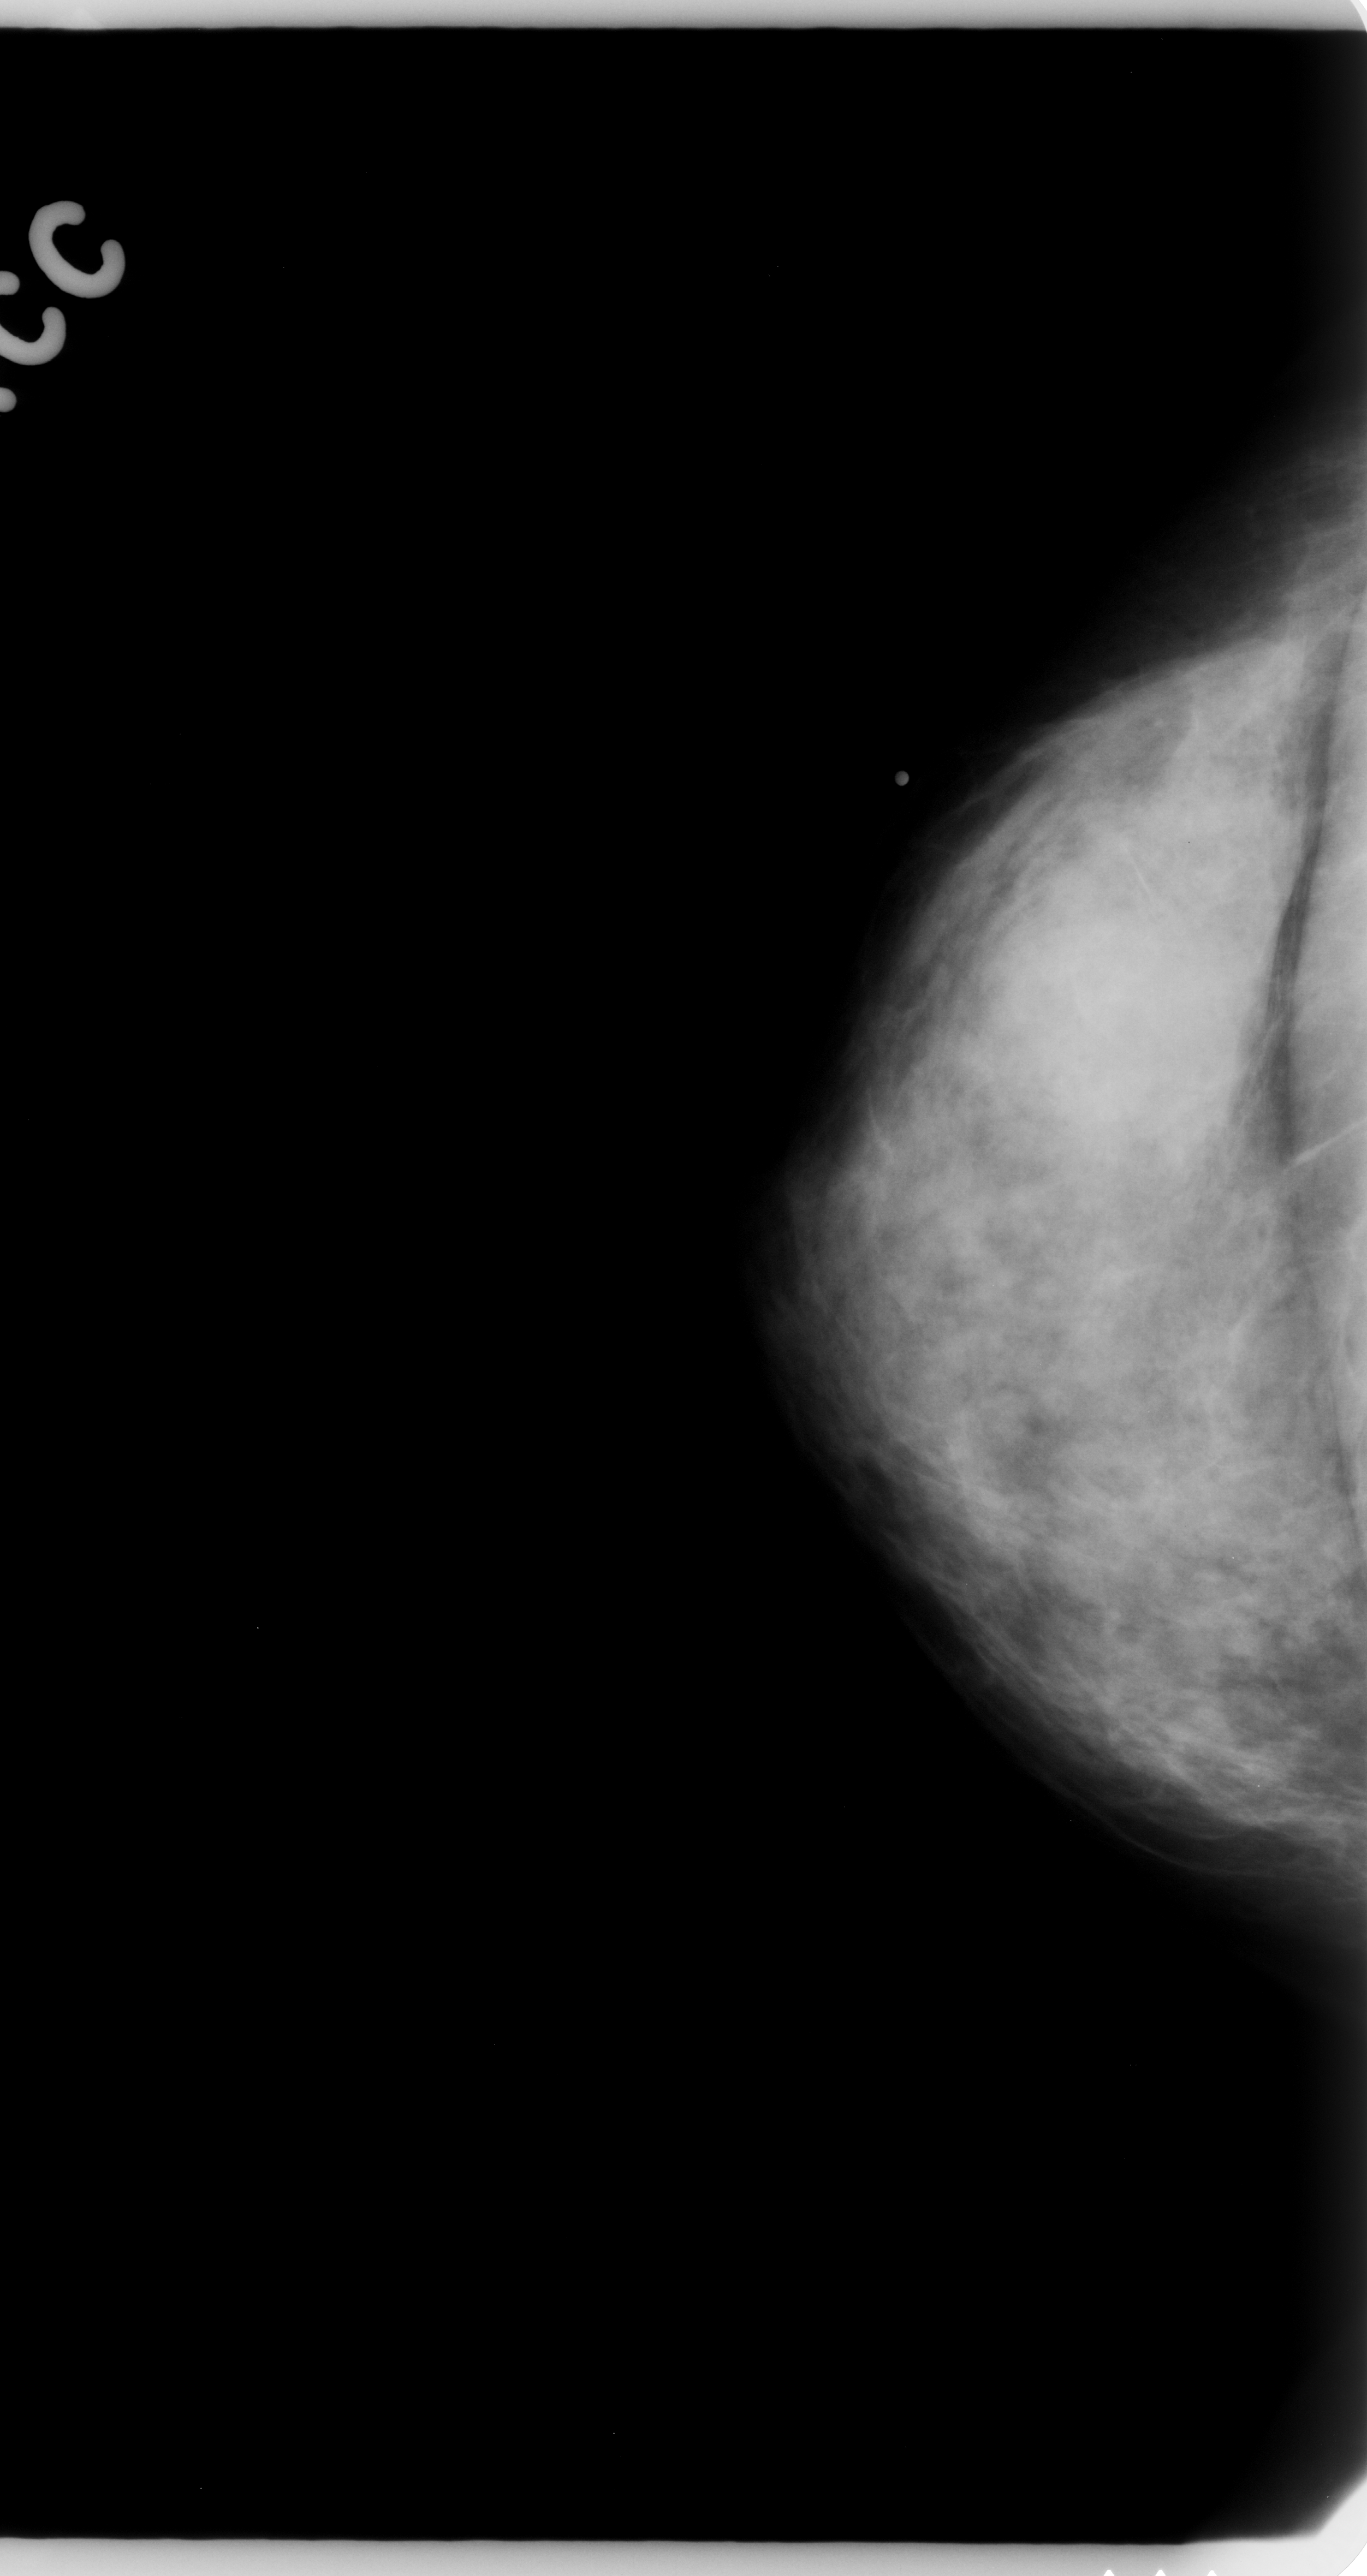
Mammogram (digitized film), right breast, CC view.
Abnormality record for this image: mass, shape round, margins ill defined; BI-RADS assessment category 4; pathology (as recorded): malignant.